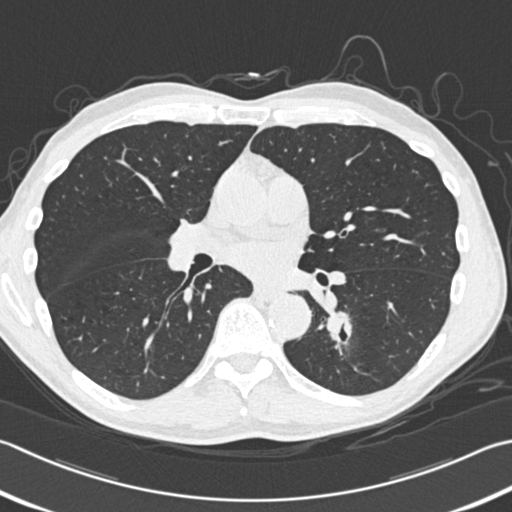
Low-dose screening chest CT, one axial slice; slice 185 of 354 in the series (ordered by position); 120 kVp; lung window (W 1500 / L -600 HU); 1 mm slice thickness; 512 × 512 image matrix, field of view 346 × 346 mm.
Annotated regions visible in this slice (outlined manually by an expert reader):
- lesion 1 (tumor, lower lobe of left lung): bounding box [x1, y1, x2, y2] px = [327, 311, 350, 342]